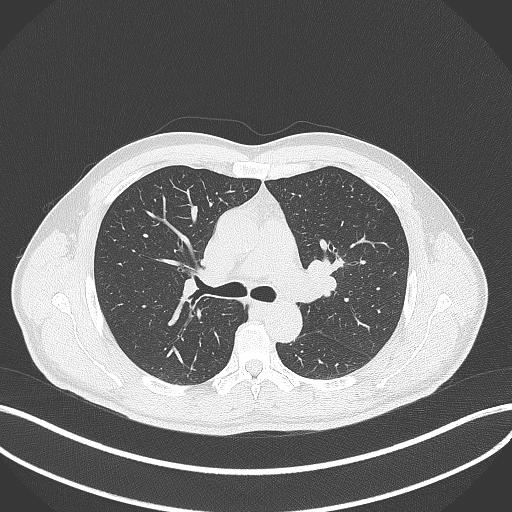
Chest CT, one axial slice. Position 271 of 392 along the scan axis. Reconstruction kernel B70f. 120 kVp. Lung window (W 1500 / L -600 HU). 1 mm slice thickness. 512 × 512 image matrix, field of view 400 × 400 mm. Patient: male, 50 years. Case-level facts recorded for this patient, not image findings: clinical TNM (as recorded): T1c N1 M1b.
Outlined on this slice (rectangle marked by the reading radiologist):
- lung tumour (recorded histology: squamous cell carcinoma): bounding box (x1, y1, x2, y2) in pixels: (330, 251, 345, 275)